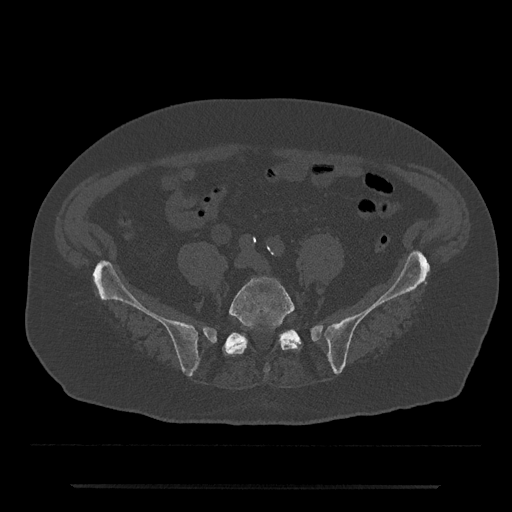
CT including the spine, one axial slice. Position 273 of 797 along the scan axis. Bone window (W 1800 / L 400 HU). 0.5 mm slice thickness. 512 × 512 image matrix, field of view 434 × 434 mm. Male patient, age 80 years. From the clinical record (not read from this slice): primary cancer: prostate; vertebrae with lytic lesions (as recorded): L1, T11.
Annotated regions visible in this slice (semi-automatically segmented with operator editing):
- L5 vertebra: box from (x=223, y=277) to (x=300, y=372) px